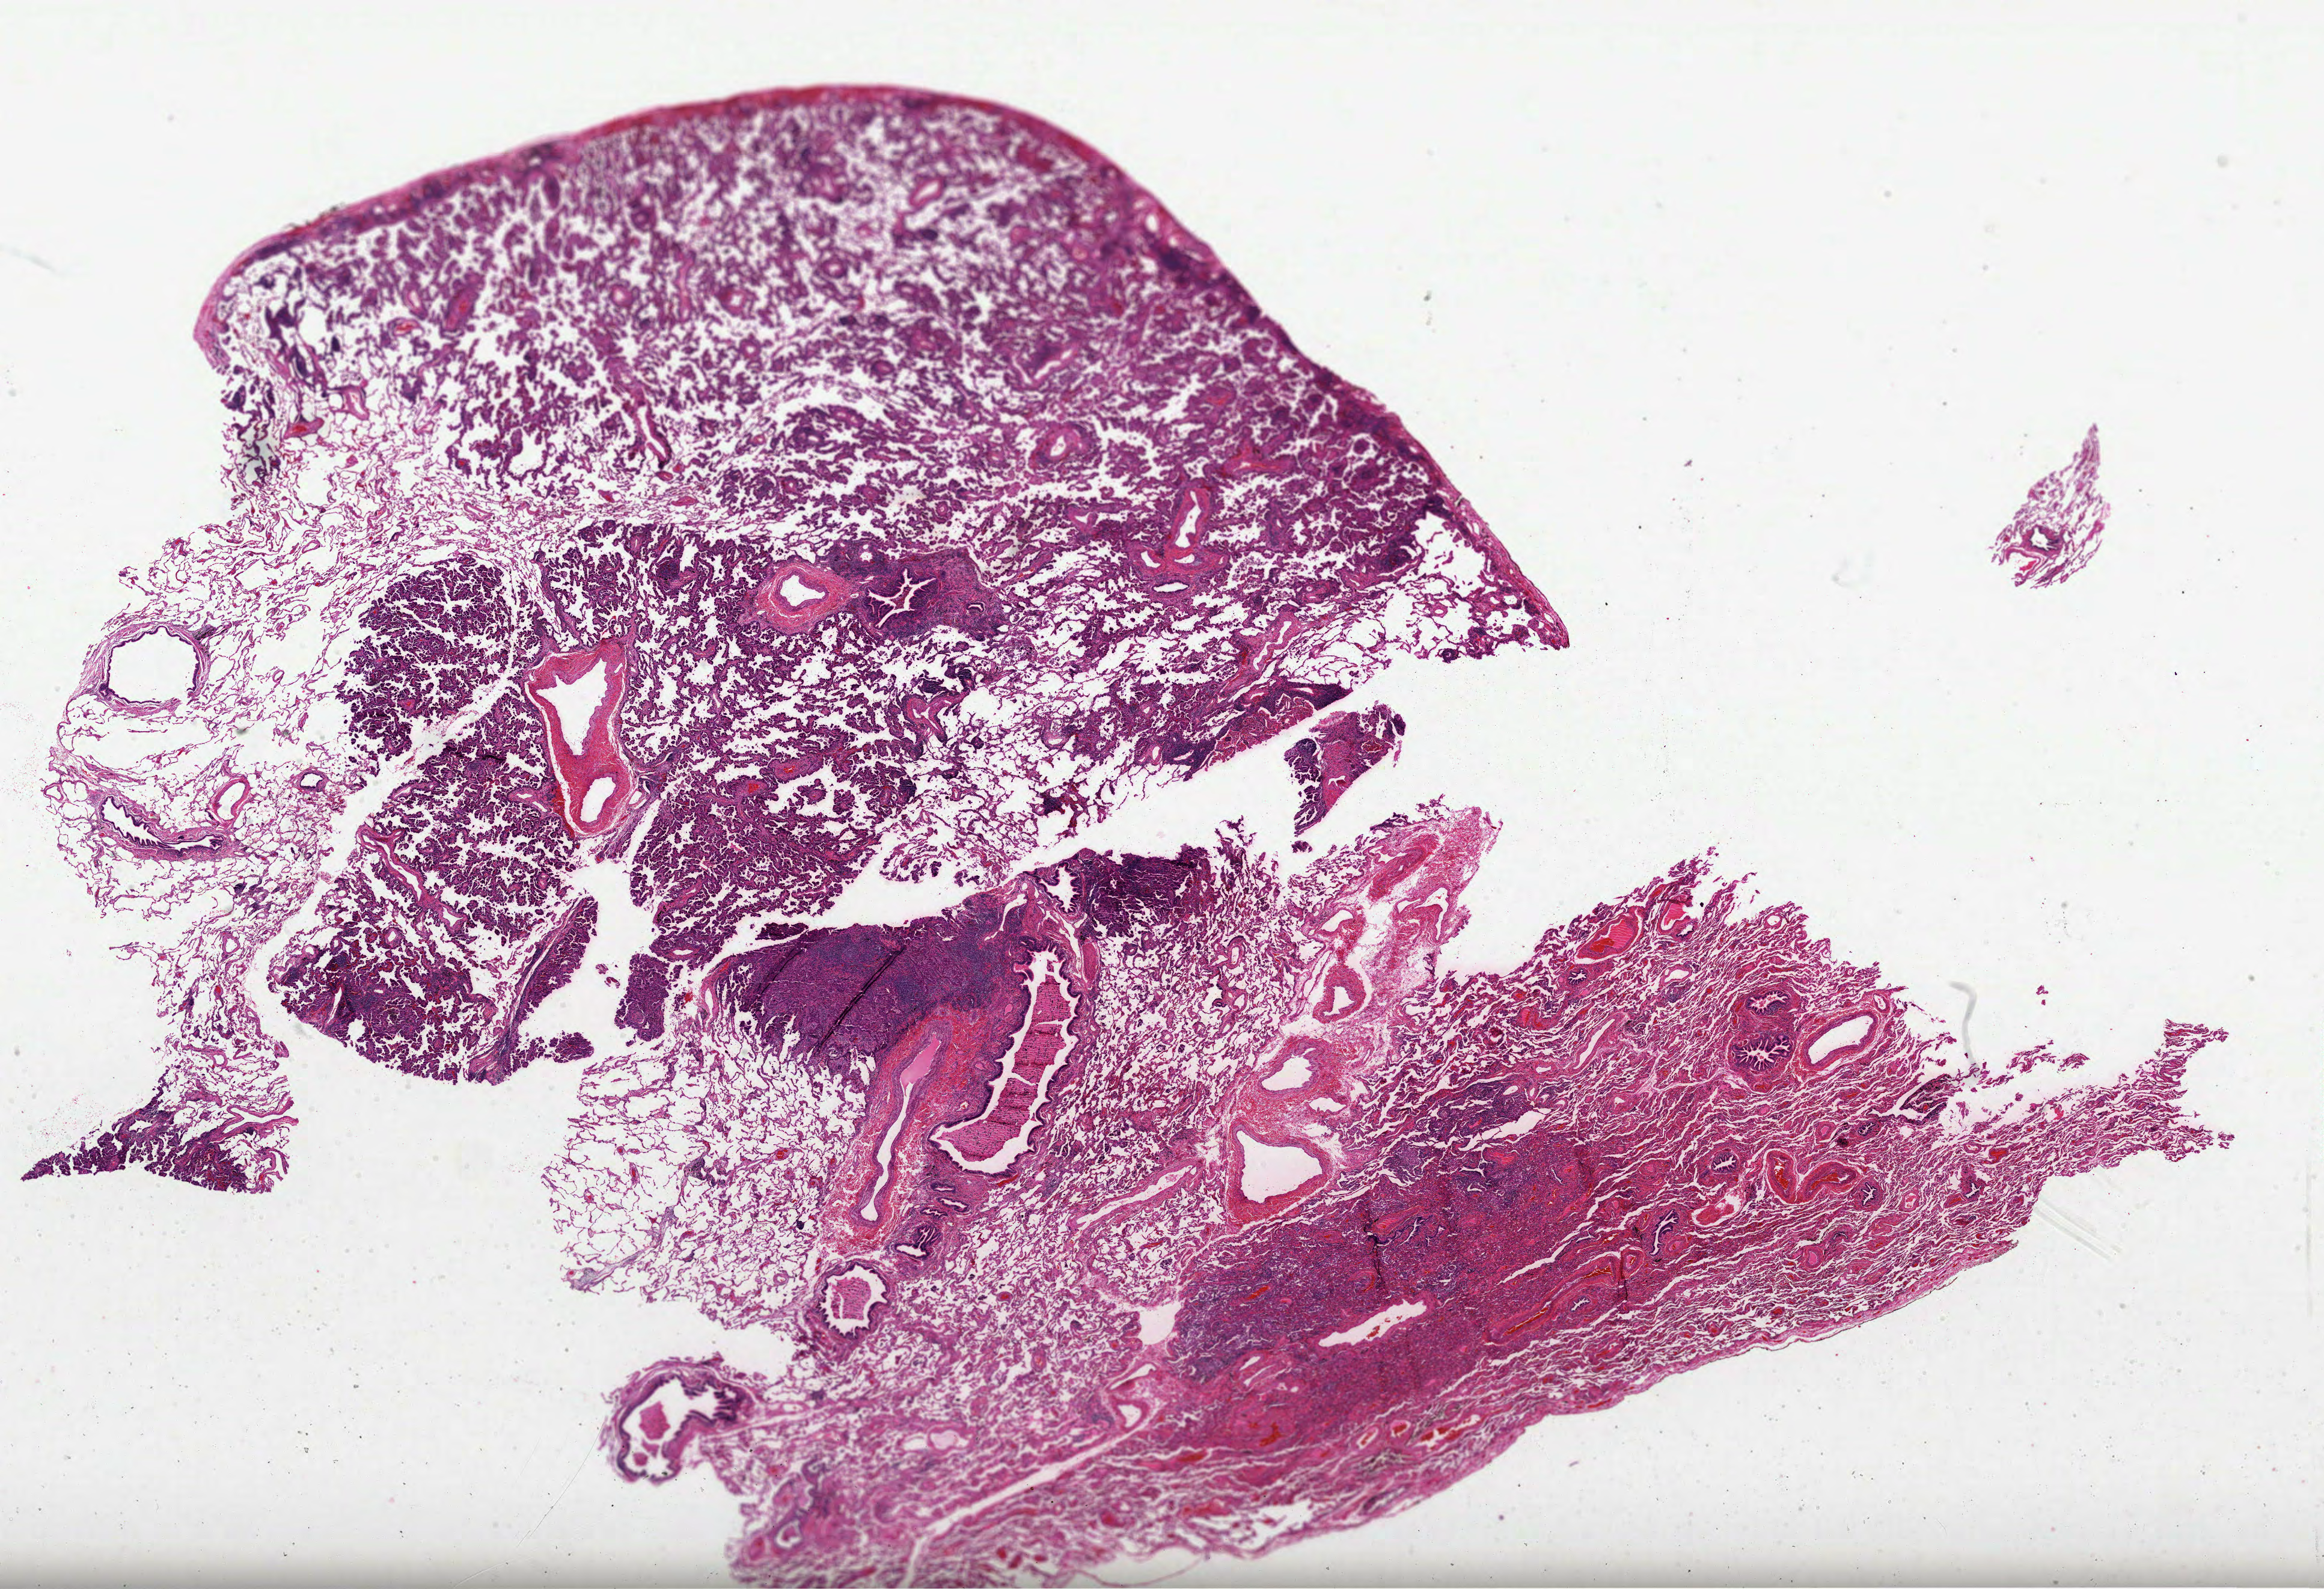
Hematoxylin and eosin (H&E) stained whole-slide image — a low-resolution overview of the entire scanned area, about 31.2 x 21.3 mm (acquisition: 40x scan); FFPE section; primary tumour sample from the lung. Patient: female, age at initial diagnosis 74 years.
AJCC pathologic stage: IA (3rd edition). Diagnosis: Adenocarcinoma, NOS (lower lobe, lung). Laterality: left.